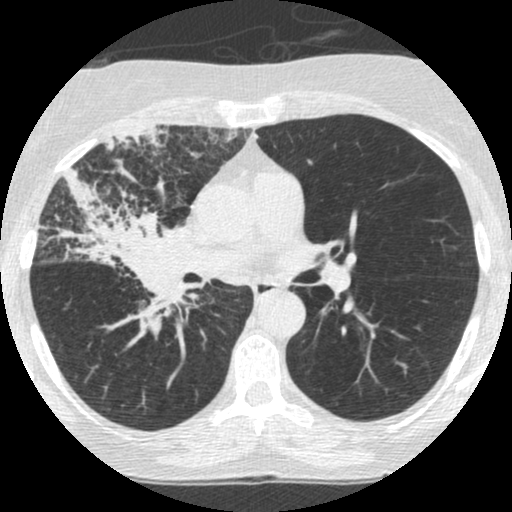
Low-dose screening chest CT, one axial slice; slice 146 of 253 in the series (ordered by position); reconstruction kernel STANDARD; lung window (W 1500 / L -600 HU); 512 × 512 image matrix, field of view 294 × 294 mm.
Annotated regions visible in this slice (expert manual segmentation):
- lesion 2 (tumor, hilum of right lung): bounding box <54,169,187,338> (left, top, right, bottom; pixels)
- lesion 3 (tumor, upper lobe of right lung): <102,126,170,157>
- lesion 4 (tumor, upper lobe of right lung): <207,127,238,145>